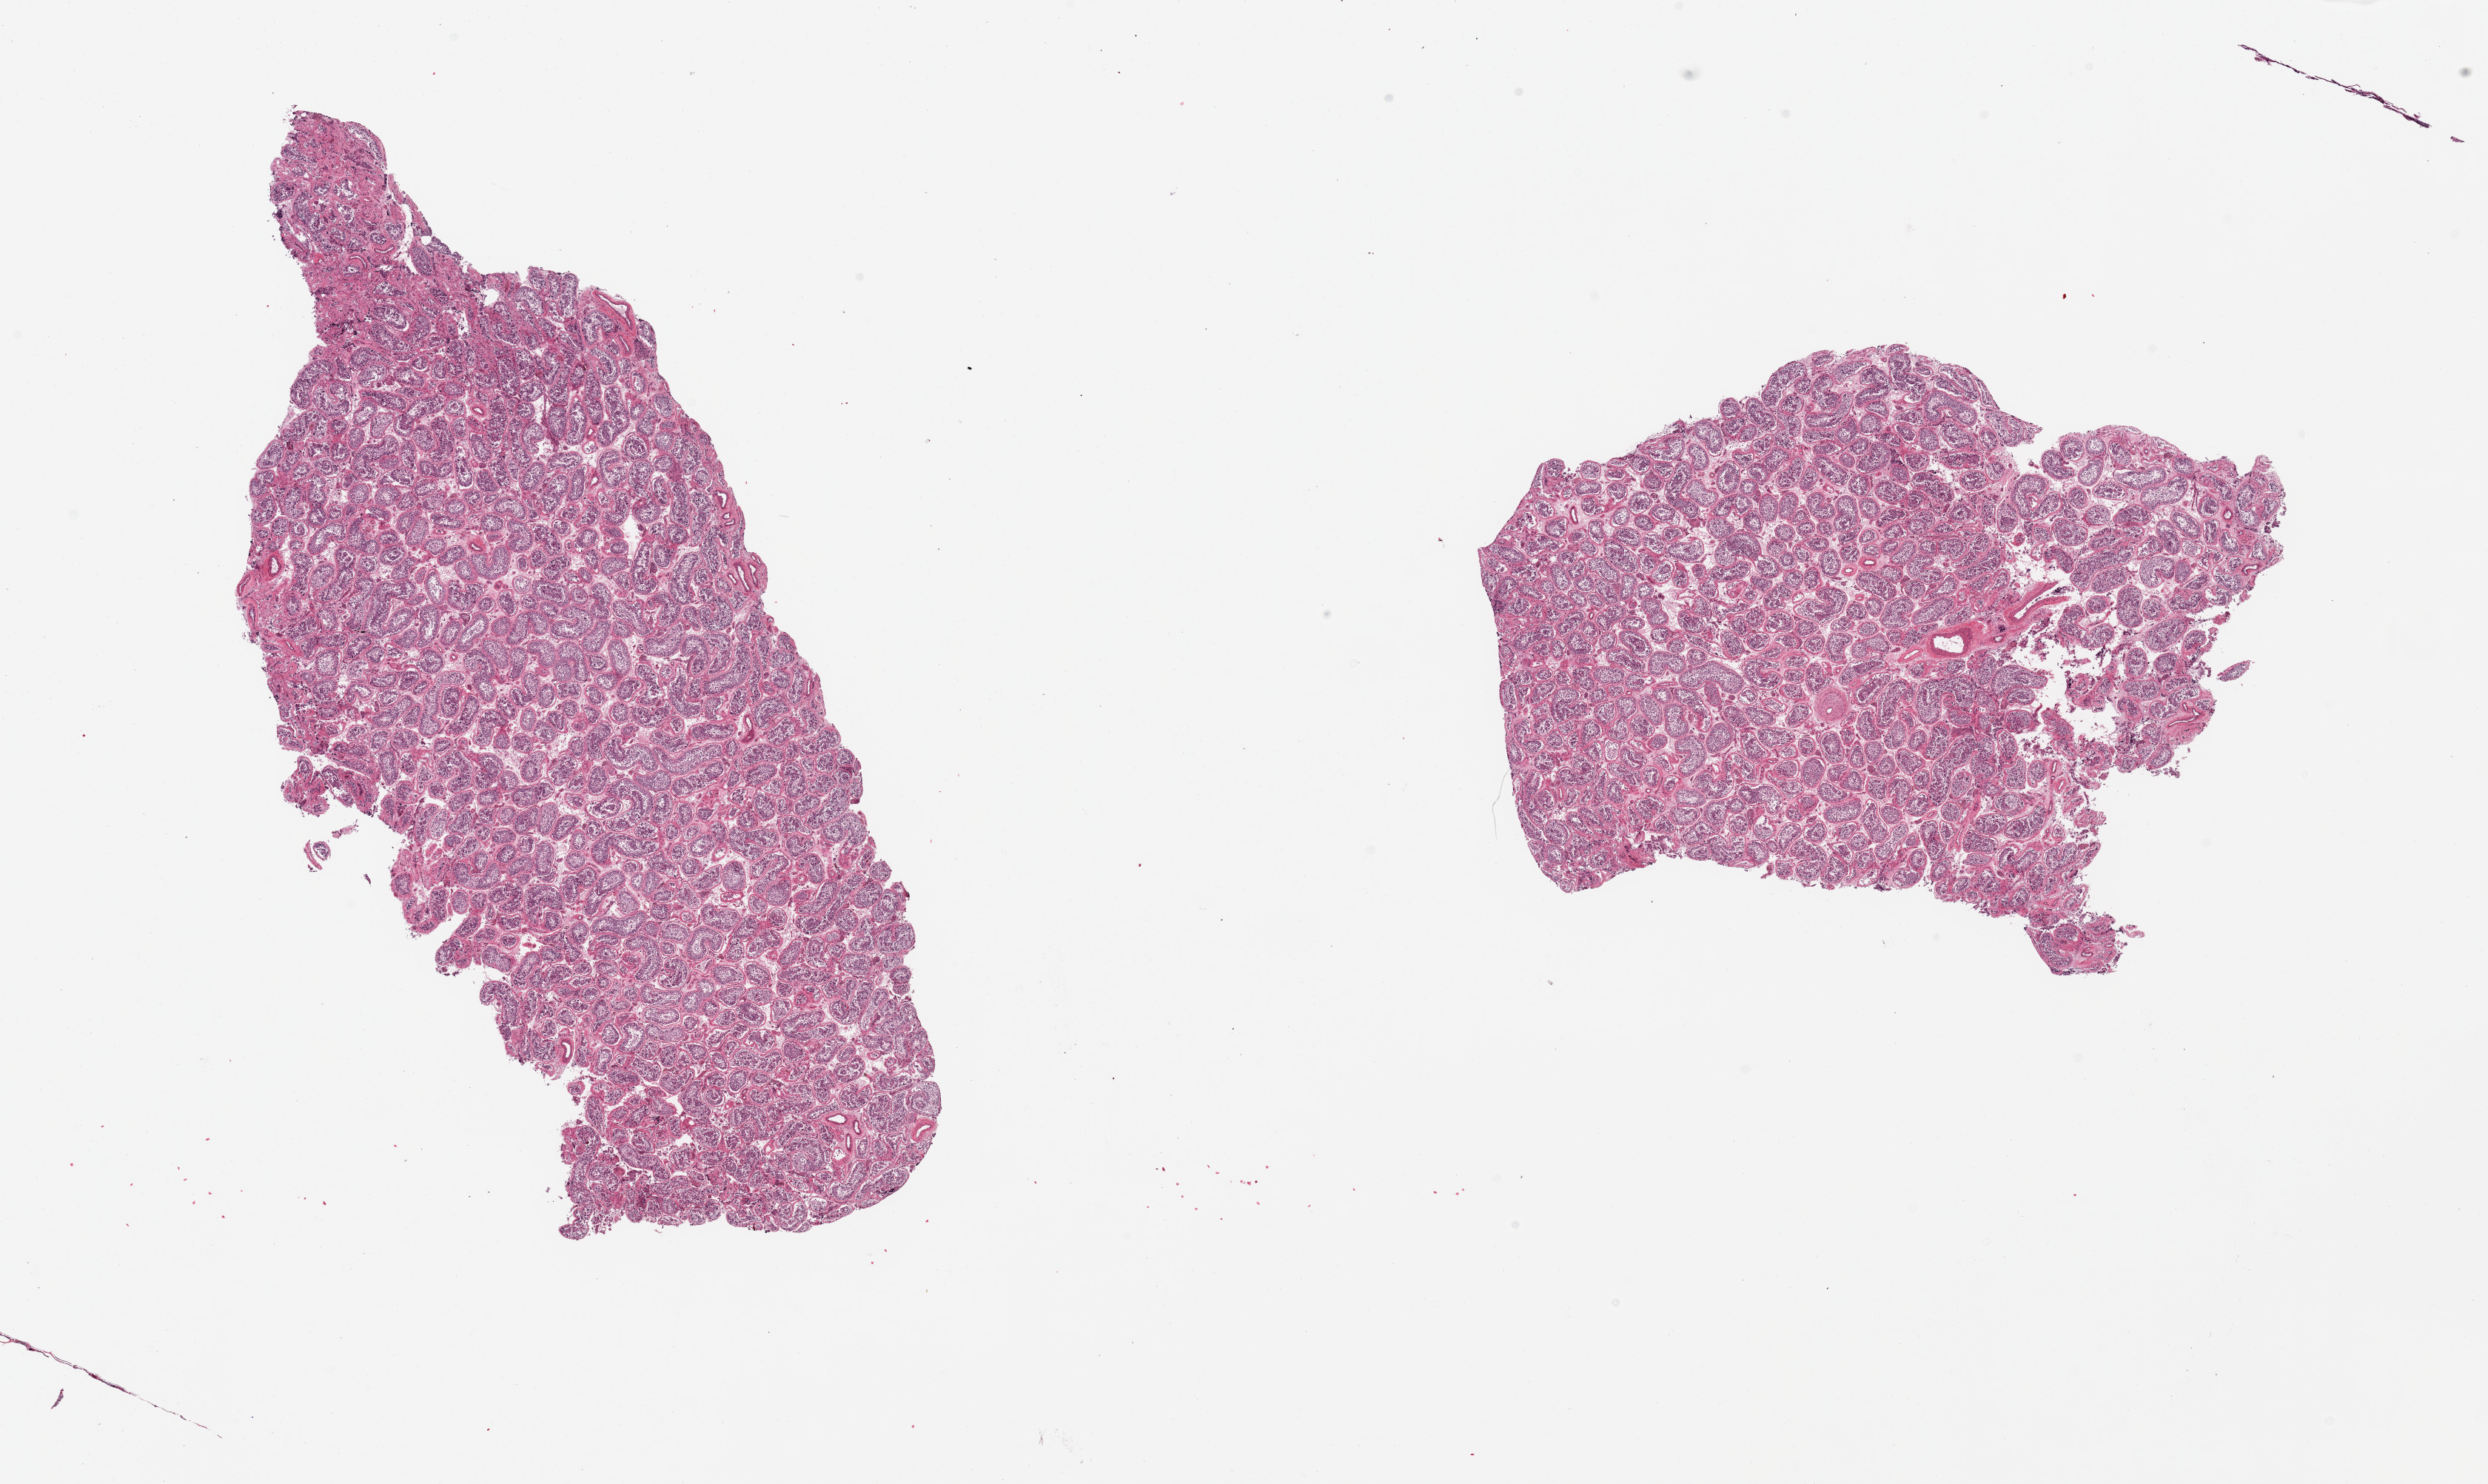
Haematoxylin and eosin whole-slide image, low-resolution overview of the scanned area, about 26.6 x 15.9 mm (from a 20x scan); PAXgene-fixed, paraffin-embedded tissue; sampled site (target tissue): testis; donor tissue sample.
• reviewer comment on this tissue sample: 2 pieces; spermatogenesis